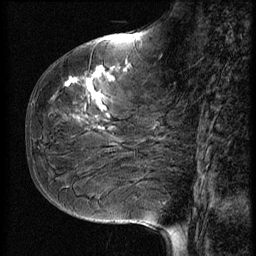
Breast MRI (dynamic contrast-enhanced), one sagittal slice; position 24 of 56 along the scan axis; 3 images stored at this slice position (order not interpretable as contrast timing); 1.5 T; TE 4.2 ms, TR 9 ms; 2.5 mm slice thickness; 256 × 256 image matrix, field of view 180 × 180 mm. Patient: female, 51 years. From the clinical record (not read from this slice): setting: breast cancer imaged before/during neoadjuvant chemotherapy; receptor status: HR-positive, HER2-negative.
Structures marked on this image (semi-automatically segmented with operator editing):
- analysis volume of interest (the breast-tissue region the enhancement analysis was run in; not a lesion): box from (x=41, y=58) to (x=167, y=161) px
- tumour enhancement mask (voxels above the 140 % enhancement threshold inside the analysis volume of interest): (x=53, y=68)–(x=108, y=129)